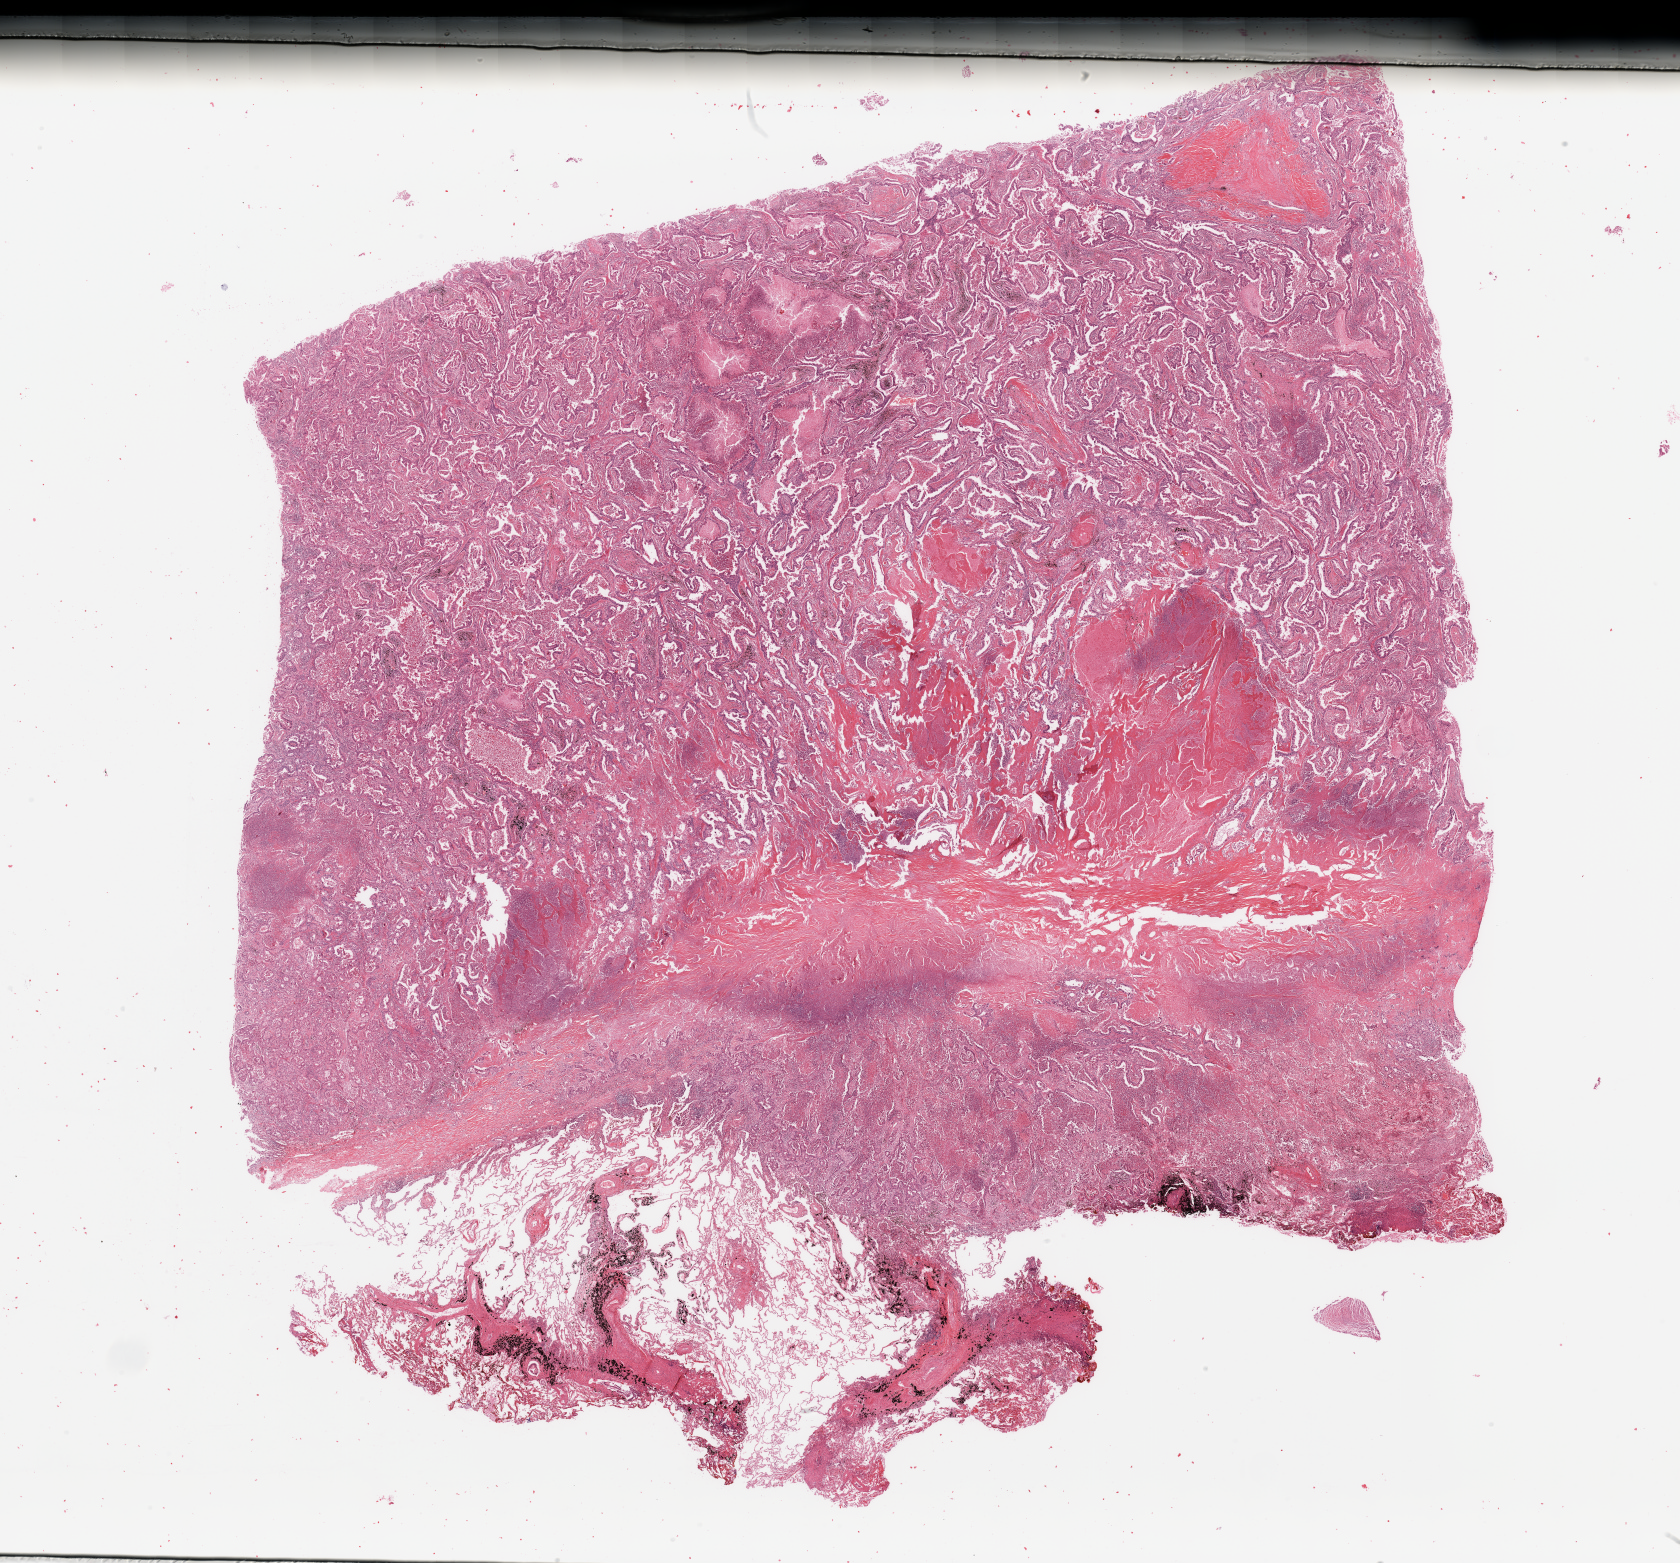
Whole-slide histology image, H&E, a low-resolution overview of the entire scanned area, about 26.6 x 24.7 mm. Lung, tumour tissue. Male, 64 y/o. Histologic grade: G2 (moderately differentiated).
• AJCC pathologic stage: IIB
• diagnosis: Adenocarcinoma, NOS